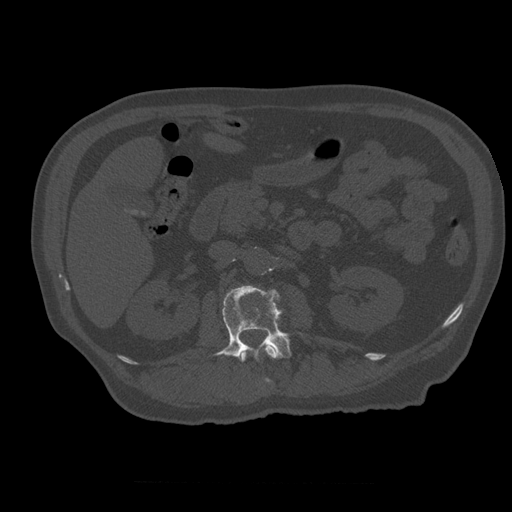
CT including the spine, one axial slice; position 218 of 399 along the scan axis; reconstruction kernel STANDARD; bone window (W 1800 / L 400 HU); 1.25 mm slice thickness; 512 × 512 image matrix, field of view 407 × 407 mm. Patient age 73 years. From the clinical record (not read from this slice): primary cancer: prostate.
Structures marked on this image (semi-automatically segmented with operator editing):
- L1 vertebra: box from (x=240, y=344) to (x=278, y=383) px
- L2 vertebra: (x=214, y=286)–(x=292, y=386)